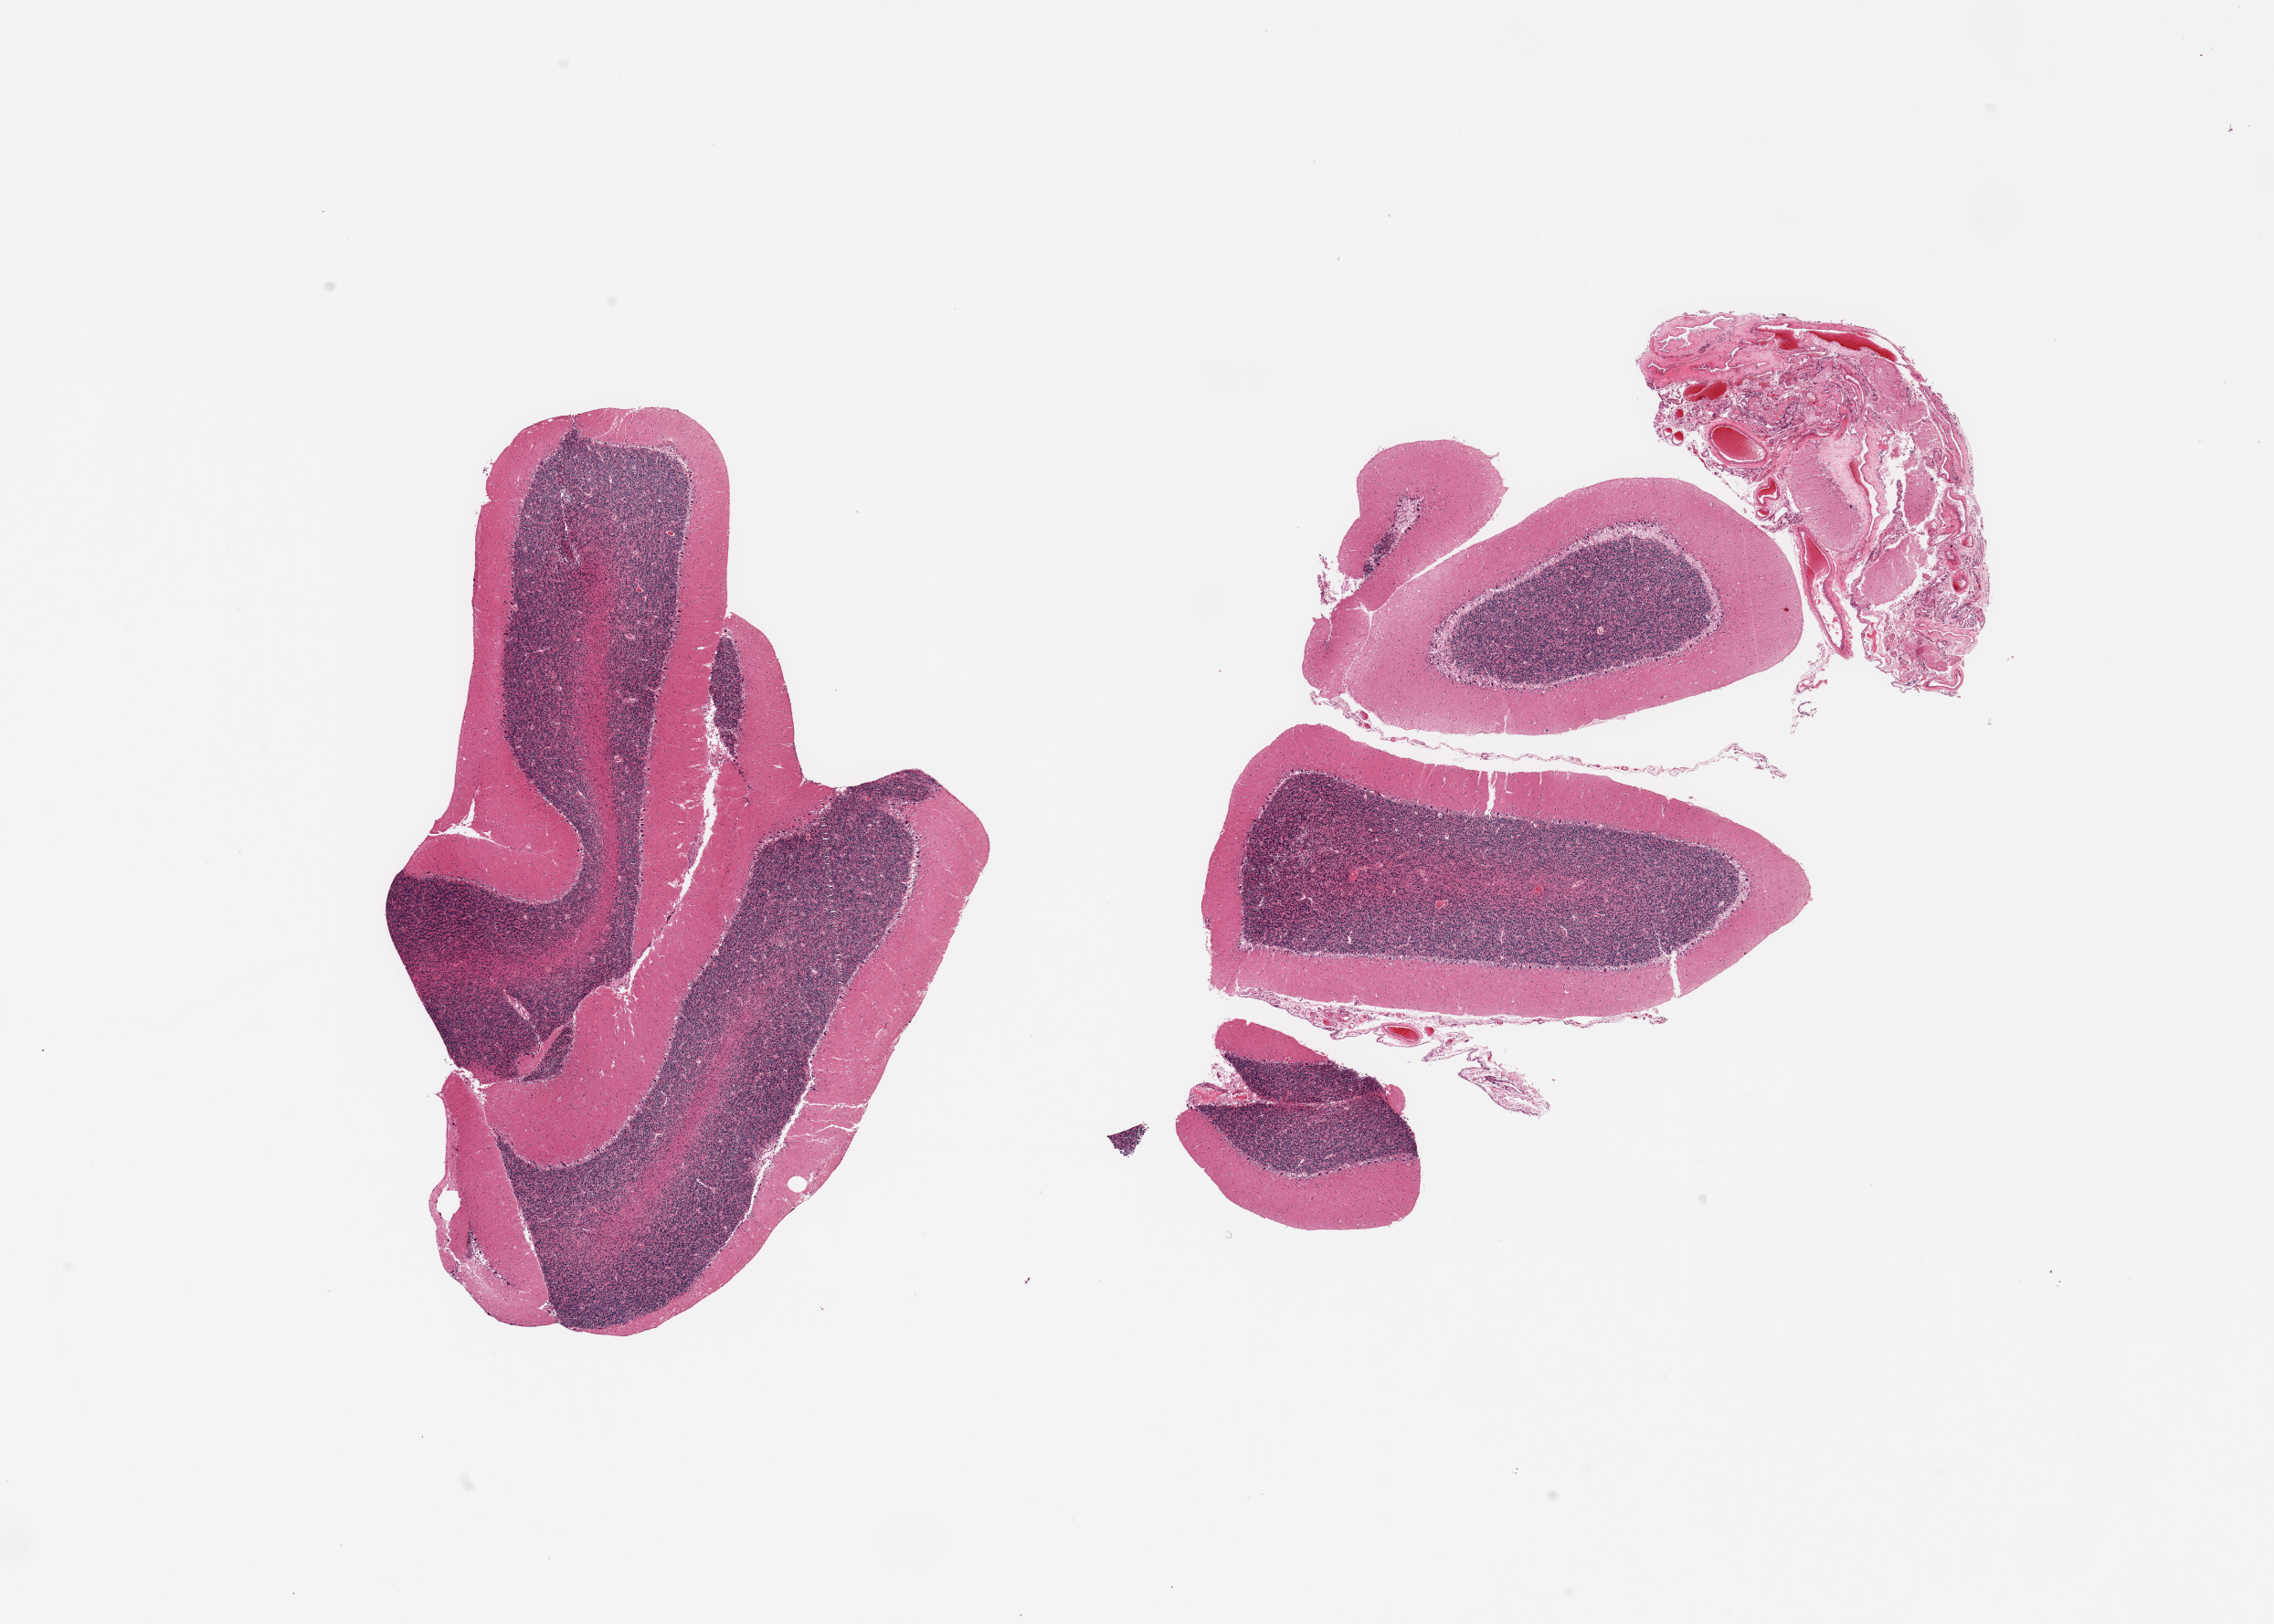
Digitized haematoxylin and eosin-stained section — a low-resolution overview of the entire scanned area, about 19.7 x 14.1 mm, PAXgene-fixed, paraffin-embedded tissue, sampled site (target tissue): cerebellum, donor tissue sample.
Review note (as recorded): 2 pieces, no abnormalities.